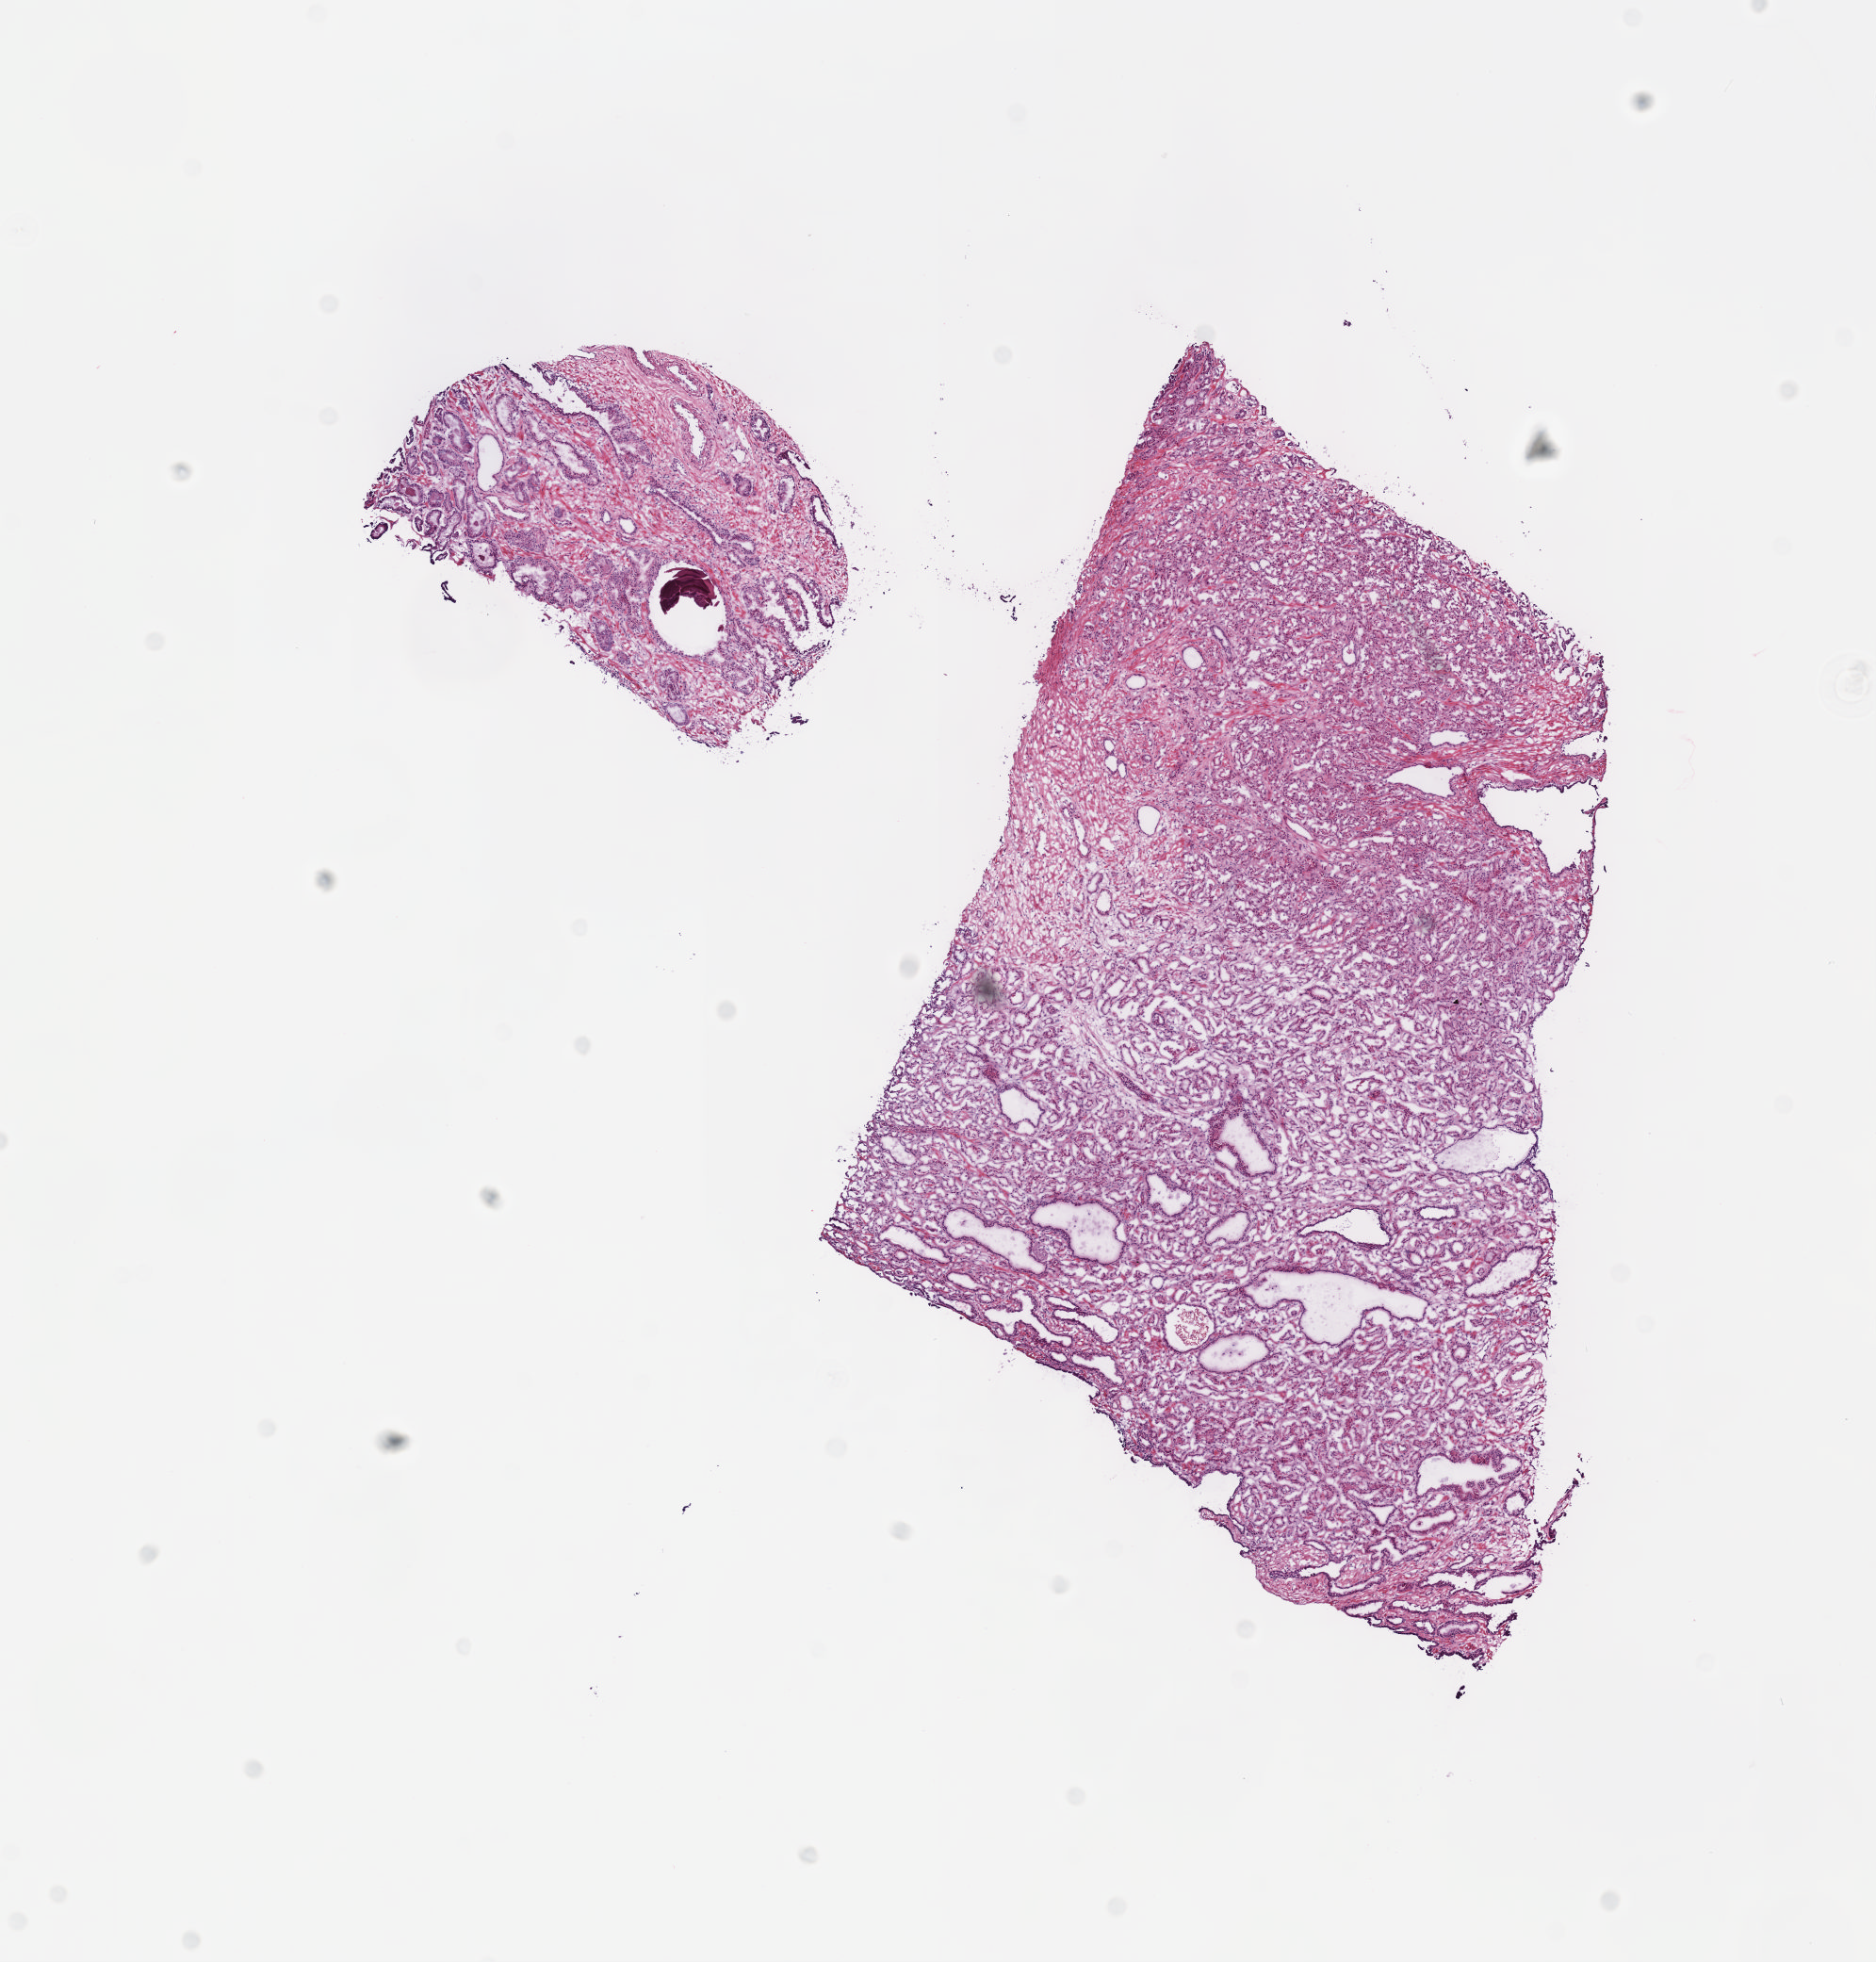
Hematoxylin and eosin (H&E) stained whole-slide image — low-resolution overview of the scanned area, about 8.1 x 8.4 mm; frozen section from the top of the tissue portion; prostate, primary tumour sample. Patient: male, age at initial diagnosis 63 years. Gleason score: 7 (3+4). Pathologist review of this section (percent, as recorded): tumour cells 70%, tumour nuclei 70%, normal cells 5%, stromal cells 25%, necrosis 0%. Infiltration values recorded for this section: lymphocyte infiltration 40%, monocyte infiltration 20%, neutrophil infiltration 20%.
- laterality: bilateral
- histologic diagnosis: Adenocarcinoma, NOS (prostate gland)